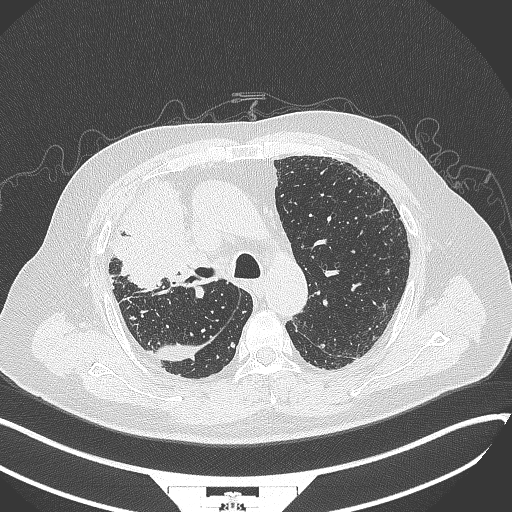
Chest CT, one axial slice. Position 247 of 384 along the scan axis. 120 kVp. Lung window (W 1500 / L -600 HU). 1 mm slice thickness. 512 × 512 image matrix. Patient: male, 69 years. Case-level facts recorded for this patient, not image findings: clinical TNM (as recorded): T4 N3 M1.
Outlined on this slice (rectangle marked by the reading radiologist):
- lung tumour (recorded histology: adenocarcinoma): box from (x=105, y=177) to (x=205, y=293) px